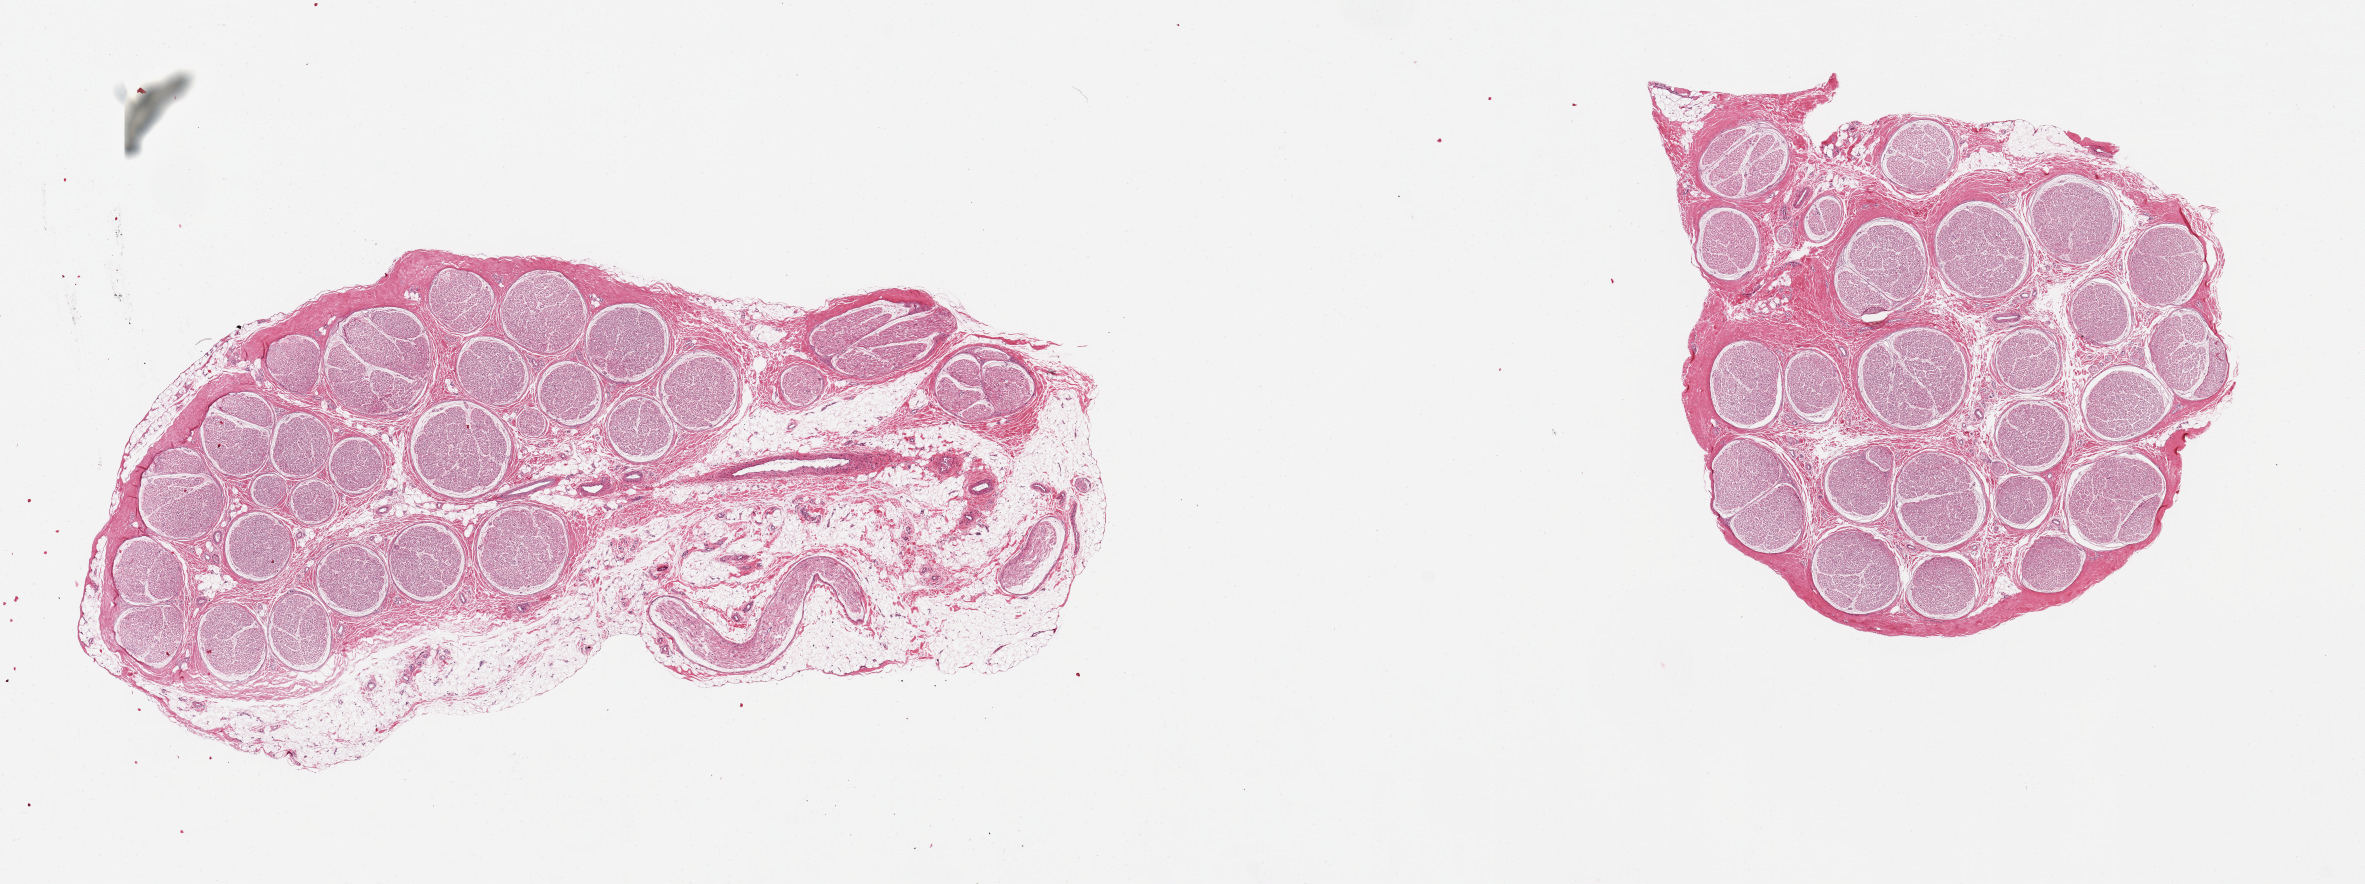
H&E whole-slide image — low-resolution overview of the scanned area, about 18.7 x 7.0 mm (from a 20x scan); PAXgene-fixed, paraffin-embedded tissue; section of tibial nerve (target tissue); donor tissue sample. Male donor.
- pathologist's review note for this sample: 2 pieces ~4mm d; Minimal adherent rim of fat on one, ~0.5mm